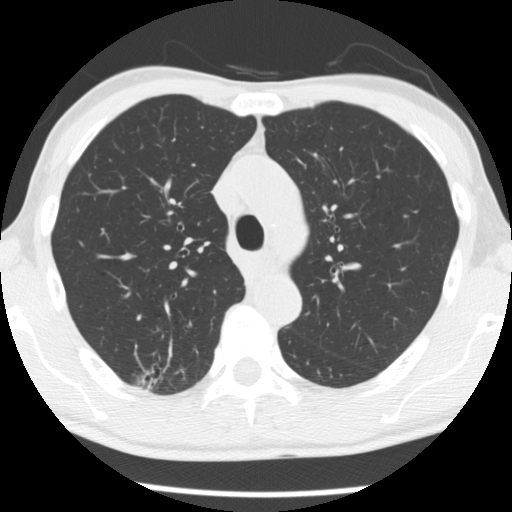
Low-dose screening chest CT, axial slice; first (baseline) screen; lung window (W 1500 / L -600 HU); 2.5 mm slice thickness; standard (soft-tissue) reconstruction kernel (STANDARD); 512 × 512 image matrix, field of view 320 × 320 mm. Male, age 66 years at enrolment.
Expert reader's lesion annotation, box from (x=132, y=356) to (x=189, y=401) px. The screening reader recorded 4 non-calcified nodules or masses ≥4 mm on this exam (right upper lobe, right upper lobe, right upper lobe, left lower lobe); which of them this box marks is not recorded. Participant outcome: lung cancer diagnosed 503 days after this screen — adenocarcinoma, NOS, right upper lobe, undifferentiated (G4), stage IA (AJCC 6th edition), 20 mm at pathology.